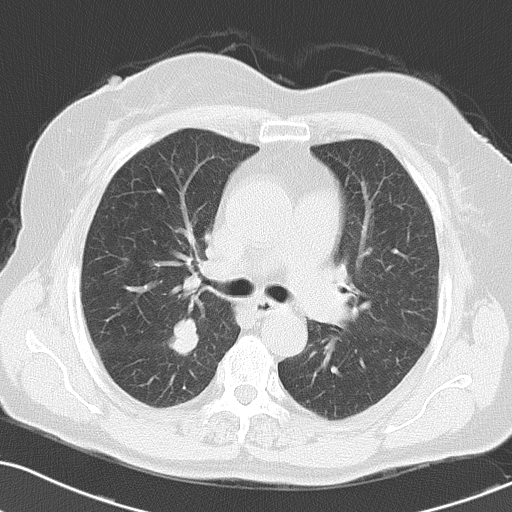
Chest CT, one axial slice. Reconstruction kernel B70f. 120 kVp. Lung window (W 1500 / L -600 HU). 5 mm slice thickness. 512 × 512 image matrix, field of view 323 × 323 mm. Female patient, age 70 years. From the clinical record (not read from this slice): clinical TNM (as recorded): T1c N3 M0; histopathological grade: G3.
Annotated regions visible in this slice (rectangle marked by the reading radiologist):
- lung tumour (recorded histology: small cell carcinoma): bounding box [x1, y1, x2, y2] px = [166, 311, 209, 369]